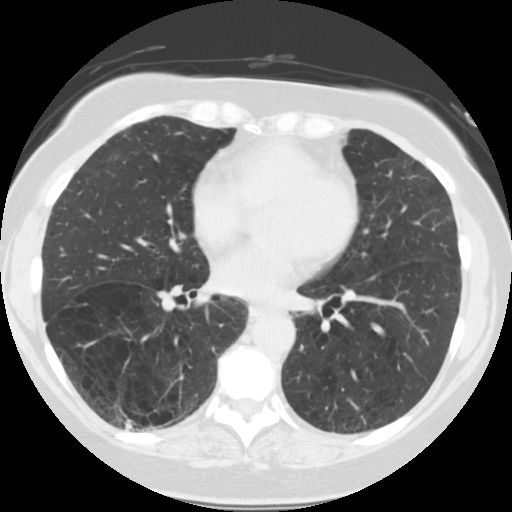
Chest CT (low-dose screening protocol), one axial image; first (baseline) screen; lung window (W 1500 / L -600 HU). Female participant, aged 59 years at enrolment. Current smoker at enrolment.
• Expert reader's lesion annotation, bounding box (x1, y1, x2, y2) in pixels: (103, 398, 156, 445).
• No non-calcified nodule or mass ≥4 mm was recorded by the screening reader at this exam.
• Participant outcome: lung cancer diagnosed 443 days after this screen (after the second annual screen) — squamous cell carcinoma, NOS, right lower lobe, poorly differentiated (G3), stage IB (AJCC 6th edition), 30 mm at pathology.